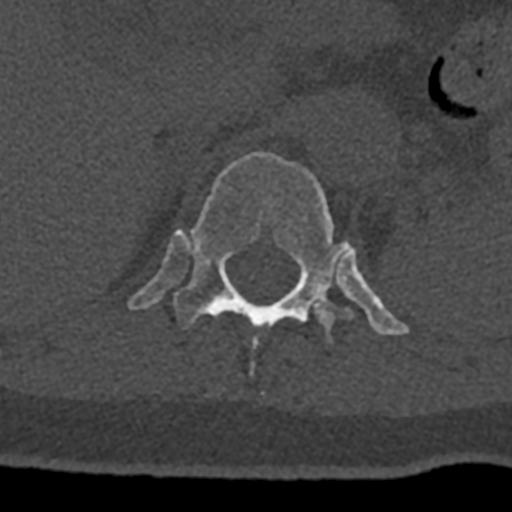
CT including the spine, one axial slice. Bone window (W 1800 / L 400 HU). 0.5 mm slice thickness. 512 × 512 image matrix, field of view 160 × 160 mm. Male patient, age 74 years. Case-level facts recorded for this patient, not image findings: primary cancer: renal.
Structures marked on this image (semi-automatically segmented with operator editing):
- T12 vertebra: box from (x=127, y=151) to (x=409, y=373) px